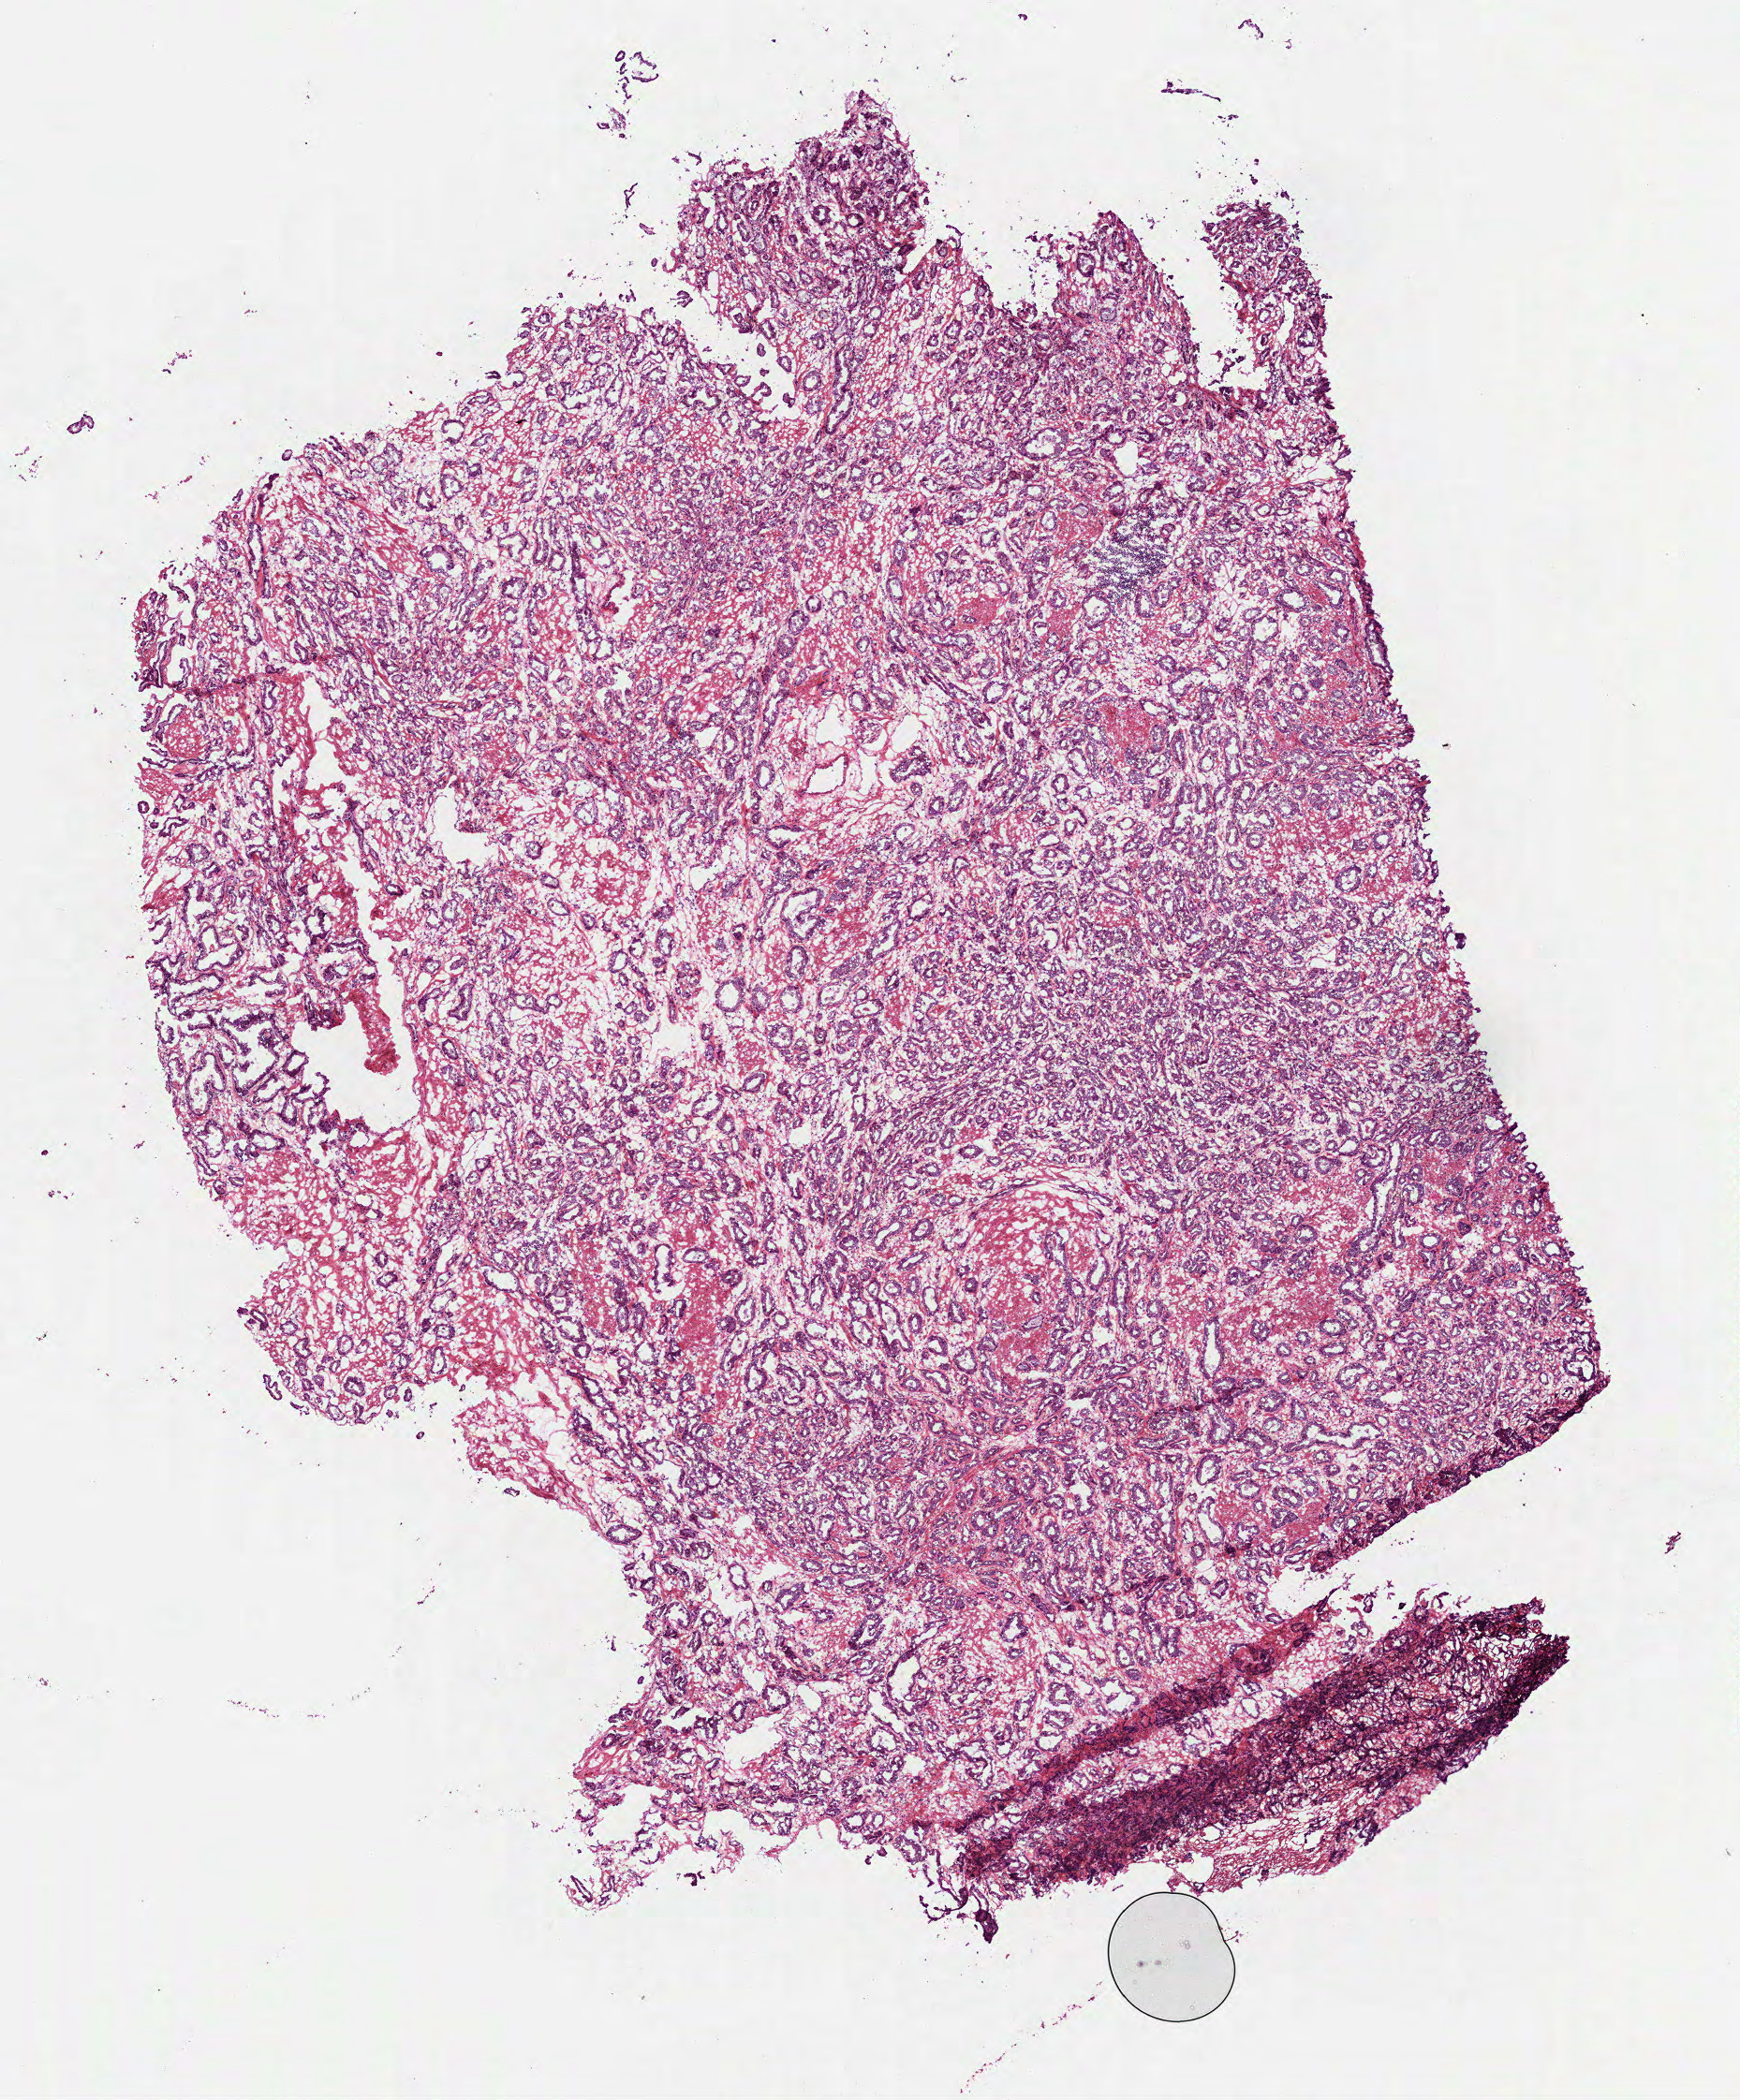
H&E whole-slide image, shown as a low-resolution overview of the whole scanned area (about 7.5 x 9.0 mm, acquisition: 40x scan), frozen section from the top of the tissue portion, primary tumour sample from the prostate. Patient: male, age at initial diagnosis 44 years. Gleason score: 7 (3+4). Pathologist review of this section (percent, as recorded): tumour cells 70%, tumour nuclei 70%, normal cells 5%, stromal cells 25%, necrosis 0%.
Laterality: bilateral. Pathologic diagnosis: Acinar cell carcinoma (prostate gland). Lymph nodes positive (case pathology): 0 of 13 examined.